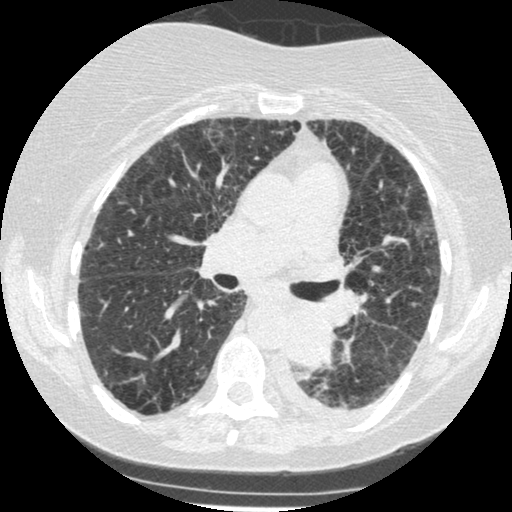
Low-dose screening chest CT, axial slice. Third annual screen. Lung window (W 1500 / L -600 HU). Standard (soft-tissue) reconstruction kernel (STANDARD). Slice 195 of 341 in the series. Female participant, aged 60 years at enrolment. Former smoker at enrolment.
• Expert-annotated lung lesion, bounding box [x1, y1, x2, y2] px = [270, 307, 342, 373].
• The exam's reader record, not a measurement of the box and not confirmed to be the same lesion: non-calcified nodule or mass ≥4 mm, left lower lobe, 54 × 38 mm, smooth margins, soft tissue attenuation, pre-existing on the prior screen: yes; interval growth: yes.
• Official screen result: positive, other.
• Lung cancer was diagnosed 15 days after this screen: small cell carcinoma, NOS, left lower lobe, undifferentiated (G4), stage IV (AJCC 6th edition), 69 mm at pathology.